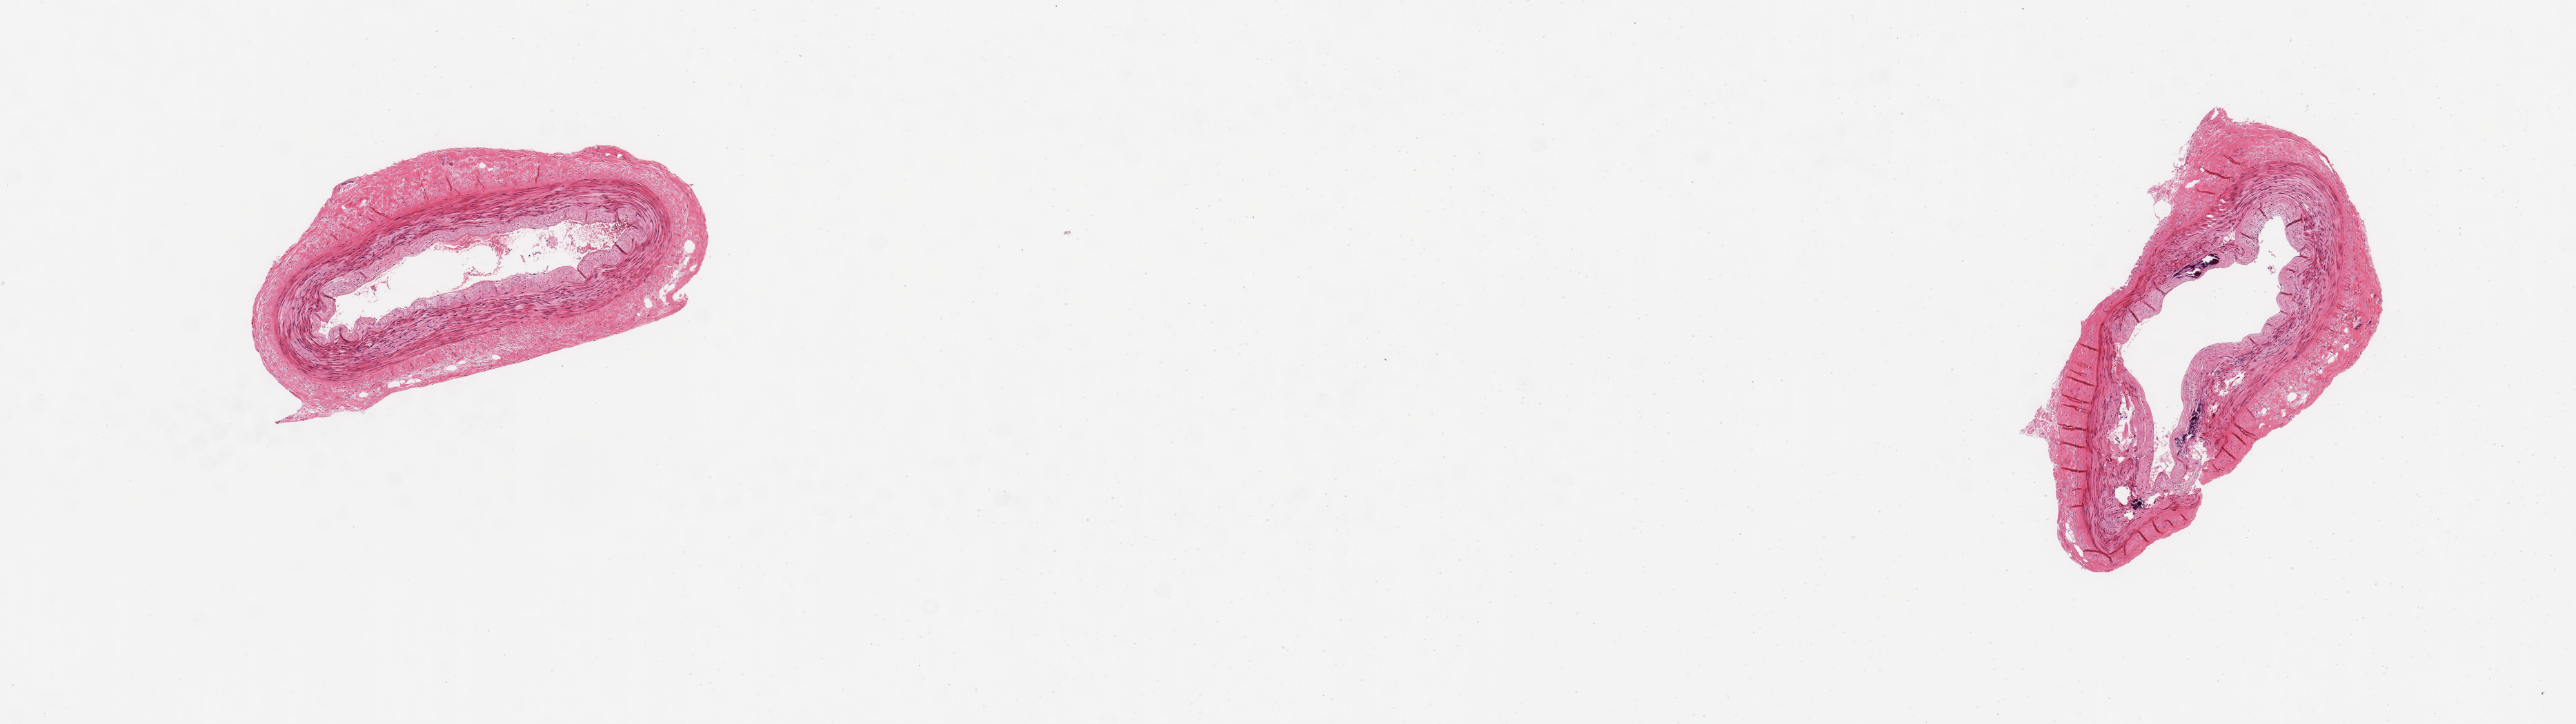
Whole-slide image, H&E stain, brightfield, shown as a low-resolution overview of the whole scanned area (about 14.8 x 4.2 mm). PAXgene-fixed, paraffin-embedded tissue. Target tissue: tibial artery. Tissue donor sample. Donor sex: female.
Reviewer comment on this tissue sample: 2 pieces; some medial calcification, mild atherosclerosis.